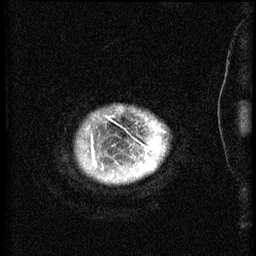
Breast MRI (dynamic contrast-enhanced), one sagittal slice; position 58 of 60 along the scan axis; 3 images stored at this slice position (order not interpretable as contrast timing); 1.5 T; TE 4.2 ms, TR 8.2 ms; 2.3 mm slice thickness; 256 × 256 image matrix, field of view 200 × 200 mm. Patient: female, 50 years.
Outlined on this slice (semi-automatically segmented with operator editing):
- analysis volume of interest (the breast-tissue region the enhancement analysis was run in; not a lesion): box from (x=82, y=116) to (x=165, y=181) px
- tumour enhancement mask (voxels above the 70 % enhancement threshold inside the analysis volume of interest): (x=92, y=148)–(x=155, y=169)